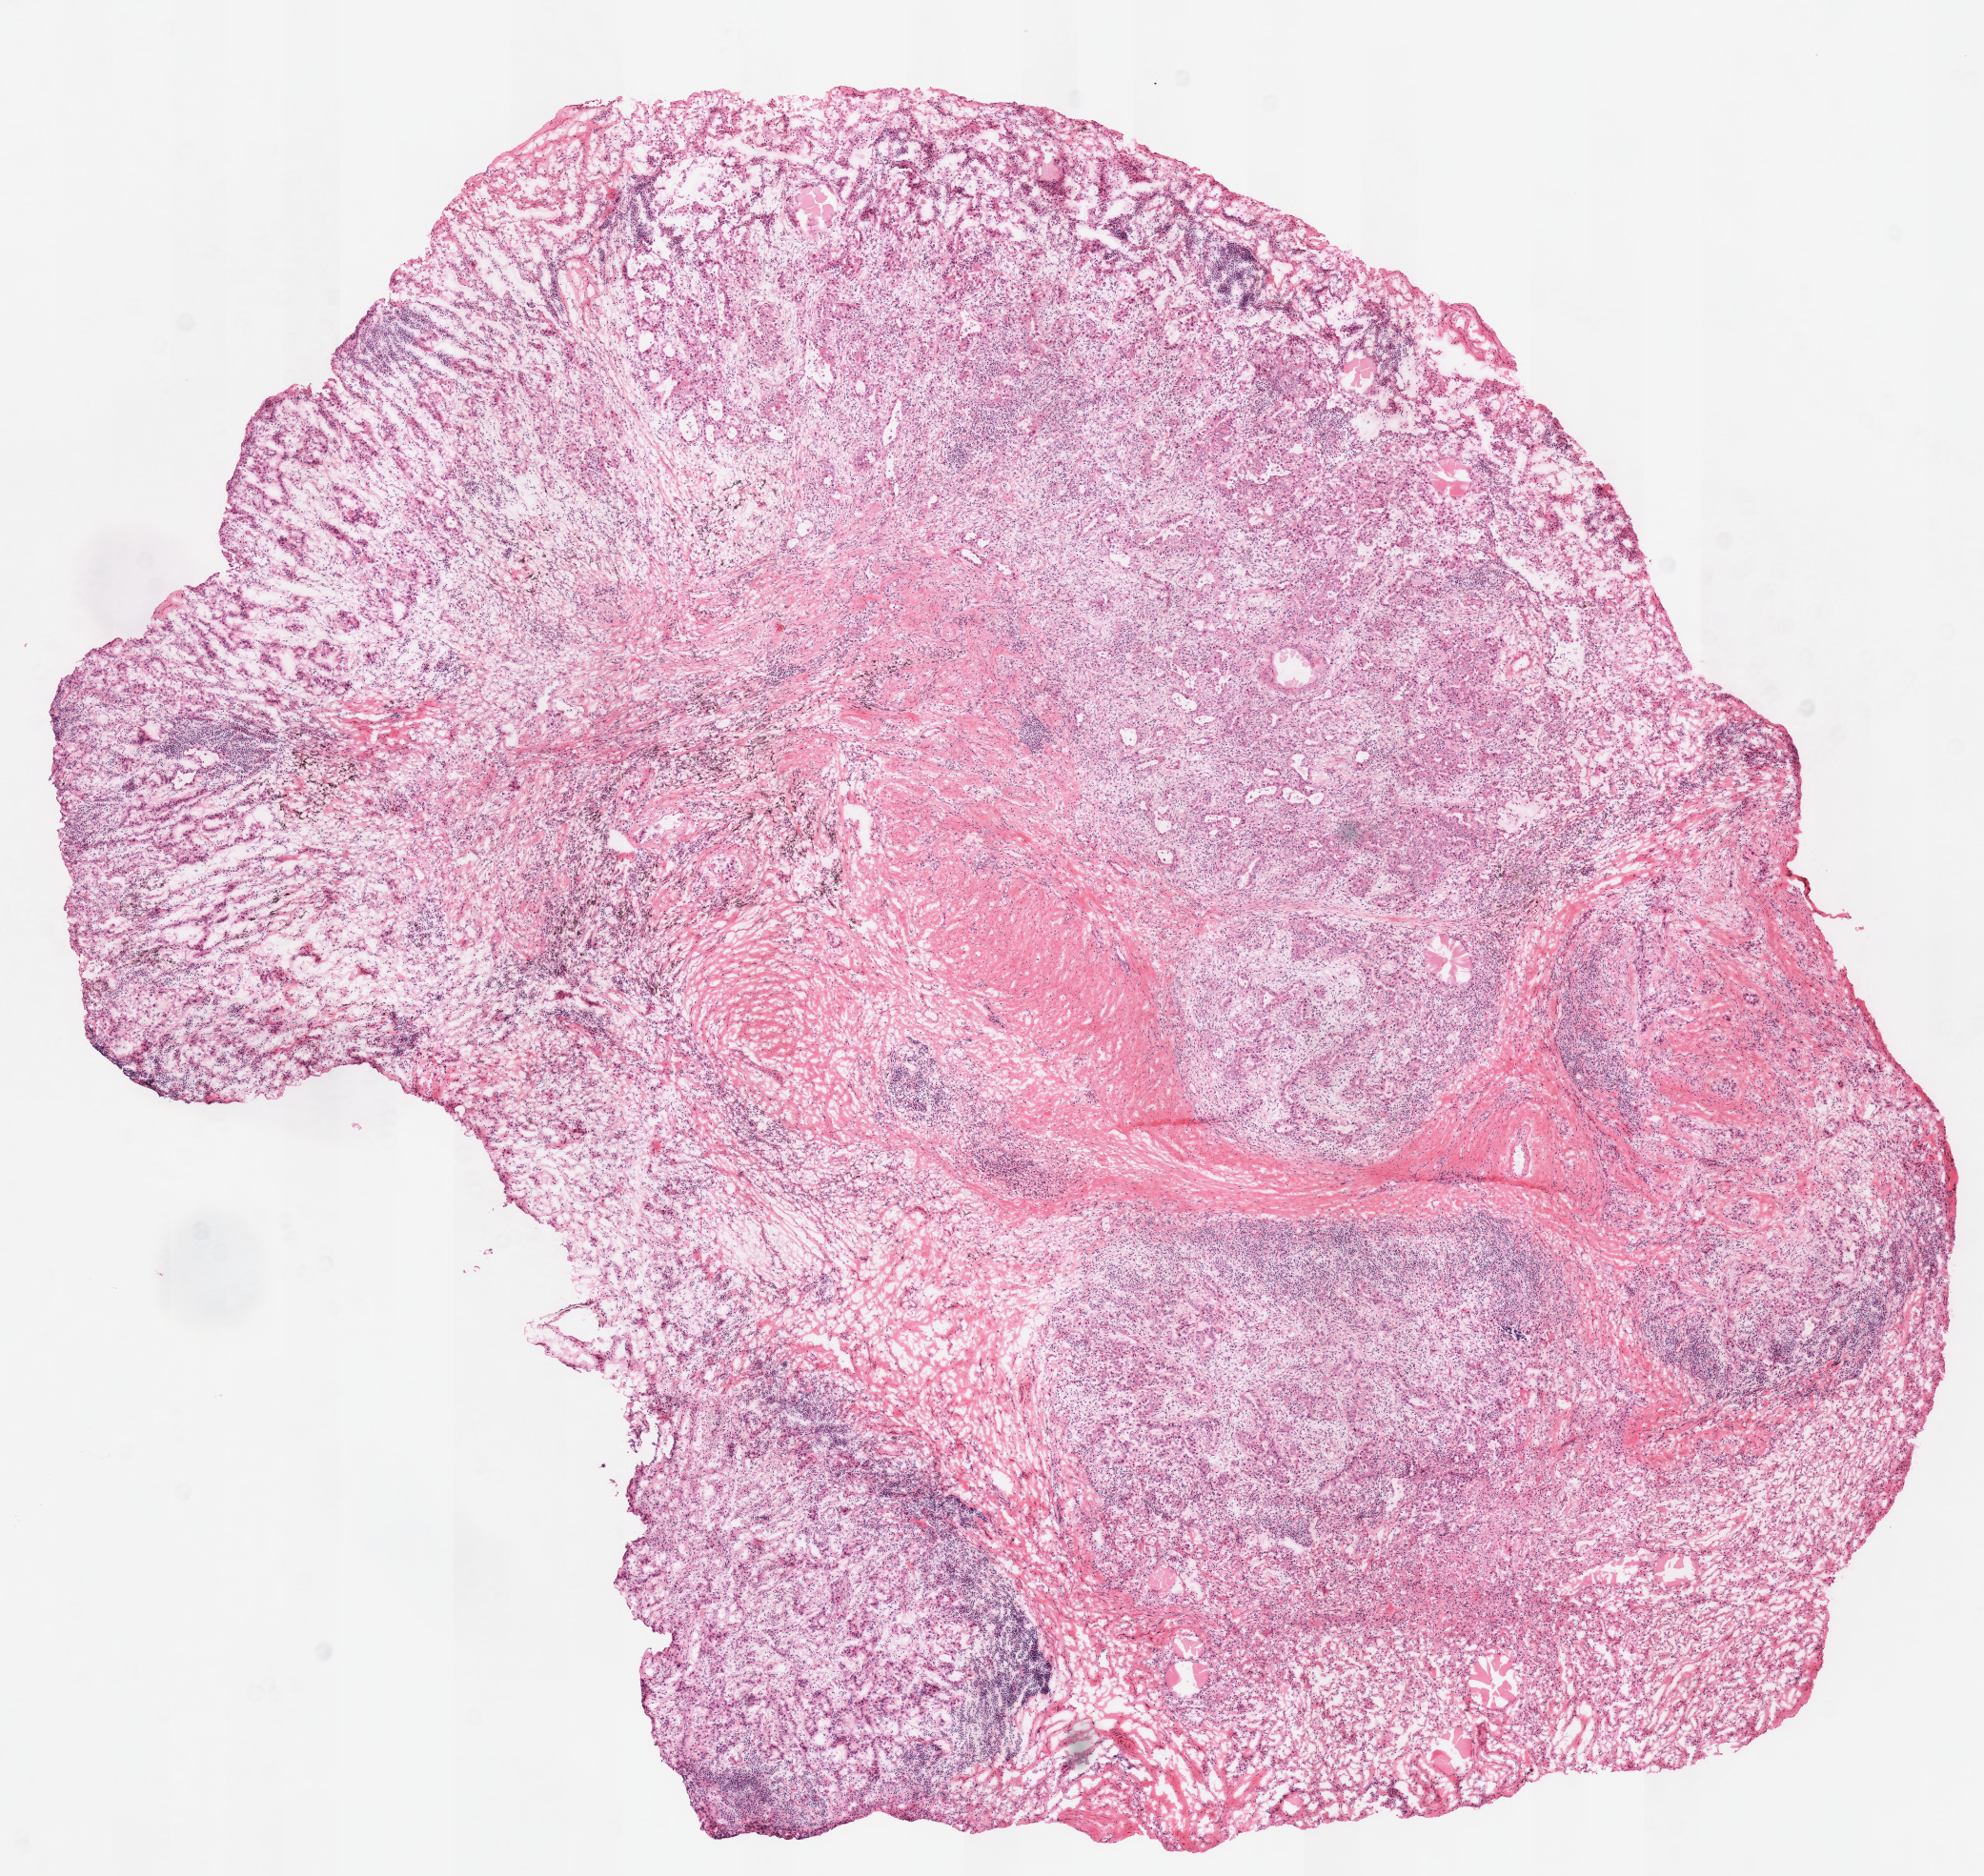
H&E-stained whole-slide image — low-resolution overview of the scanned area, about 8.2 x 7.8 mm; frozen section from the top of the tissue portion; sample: primary tumour, lung. Female, age 72 years at initial diagnosis. Slide review estimates, as recorded: tumour cells 70%, tumour nuclei 61%, normal cells 6%, stromal cells 24%, necrosis 0%. Infiltration values recorded for this section: lymphocyte infiltration 30%, monocyte infiltration 0%, neutrophil infiltration 0%.
* AJCC pathologic stage: IIB
* histologic diagnosis: Papillary adenocarcinoma, NOS (upper lobe, lung)
* TNM: T2b N1 M0